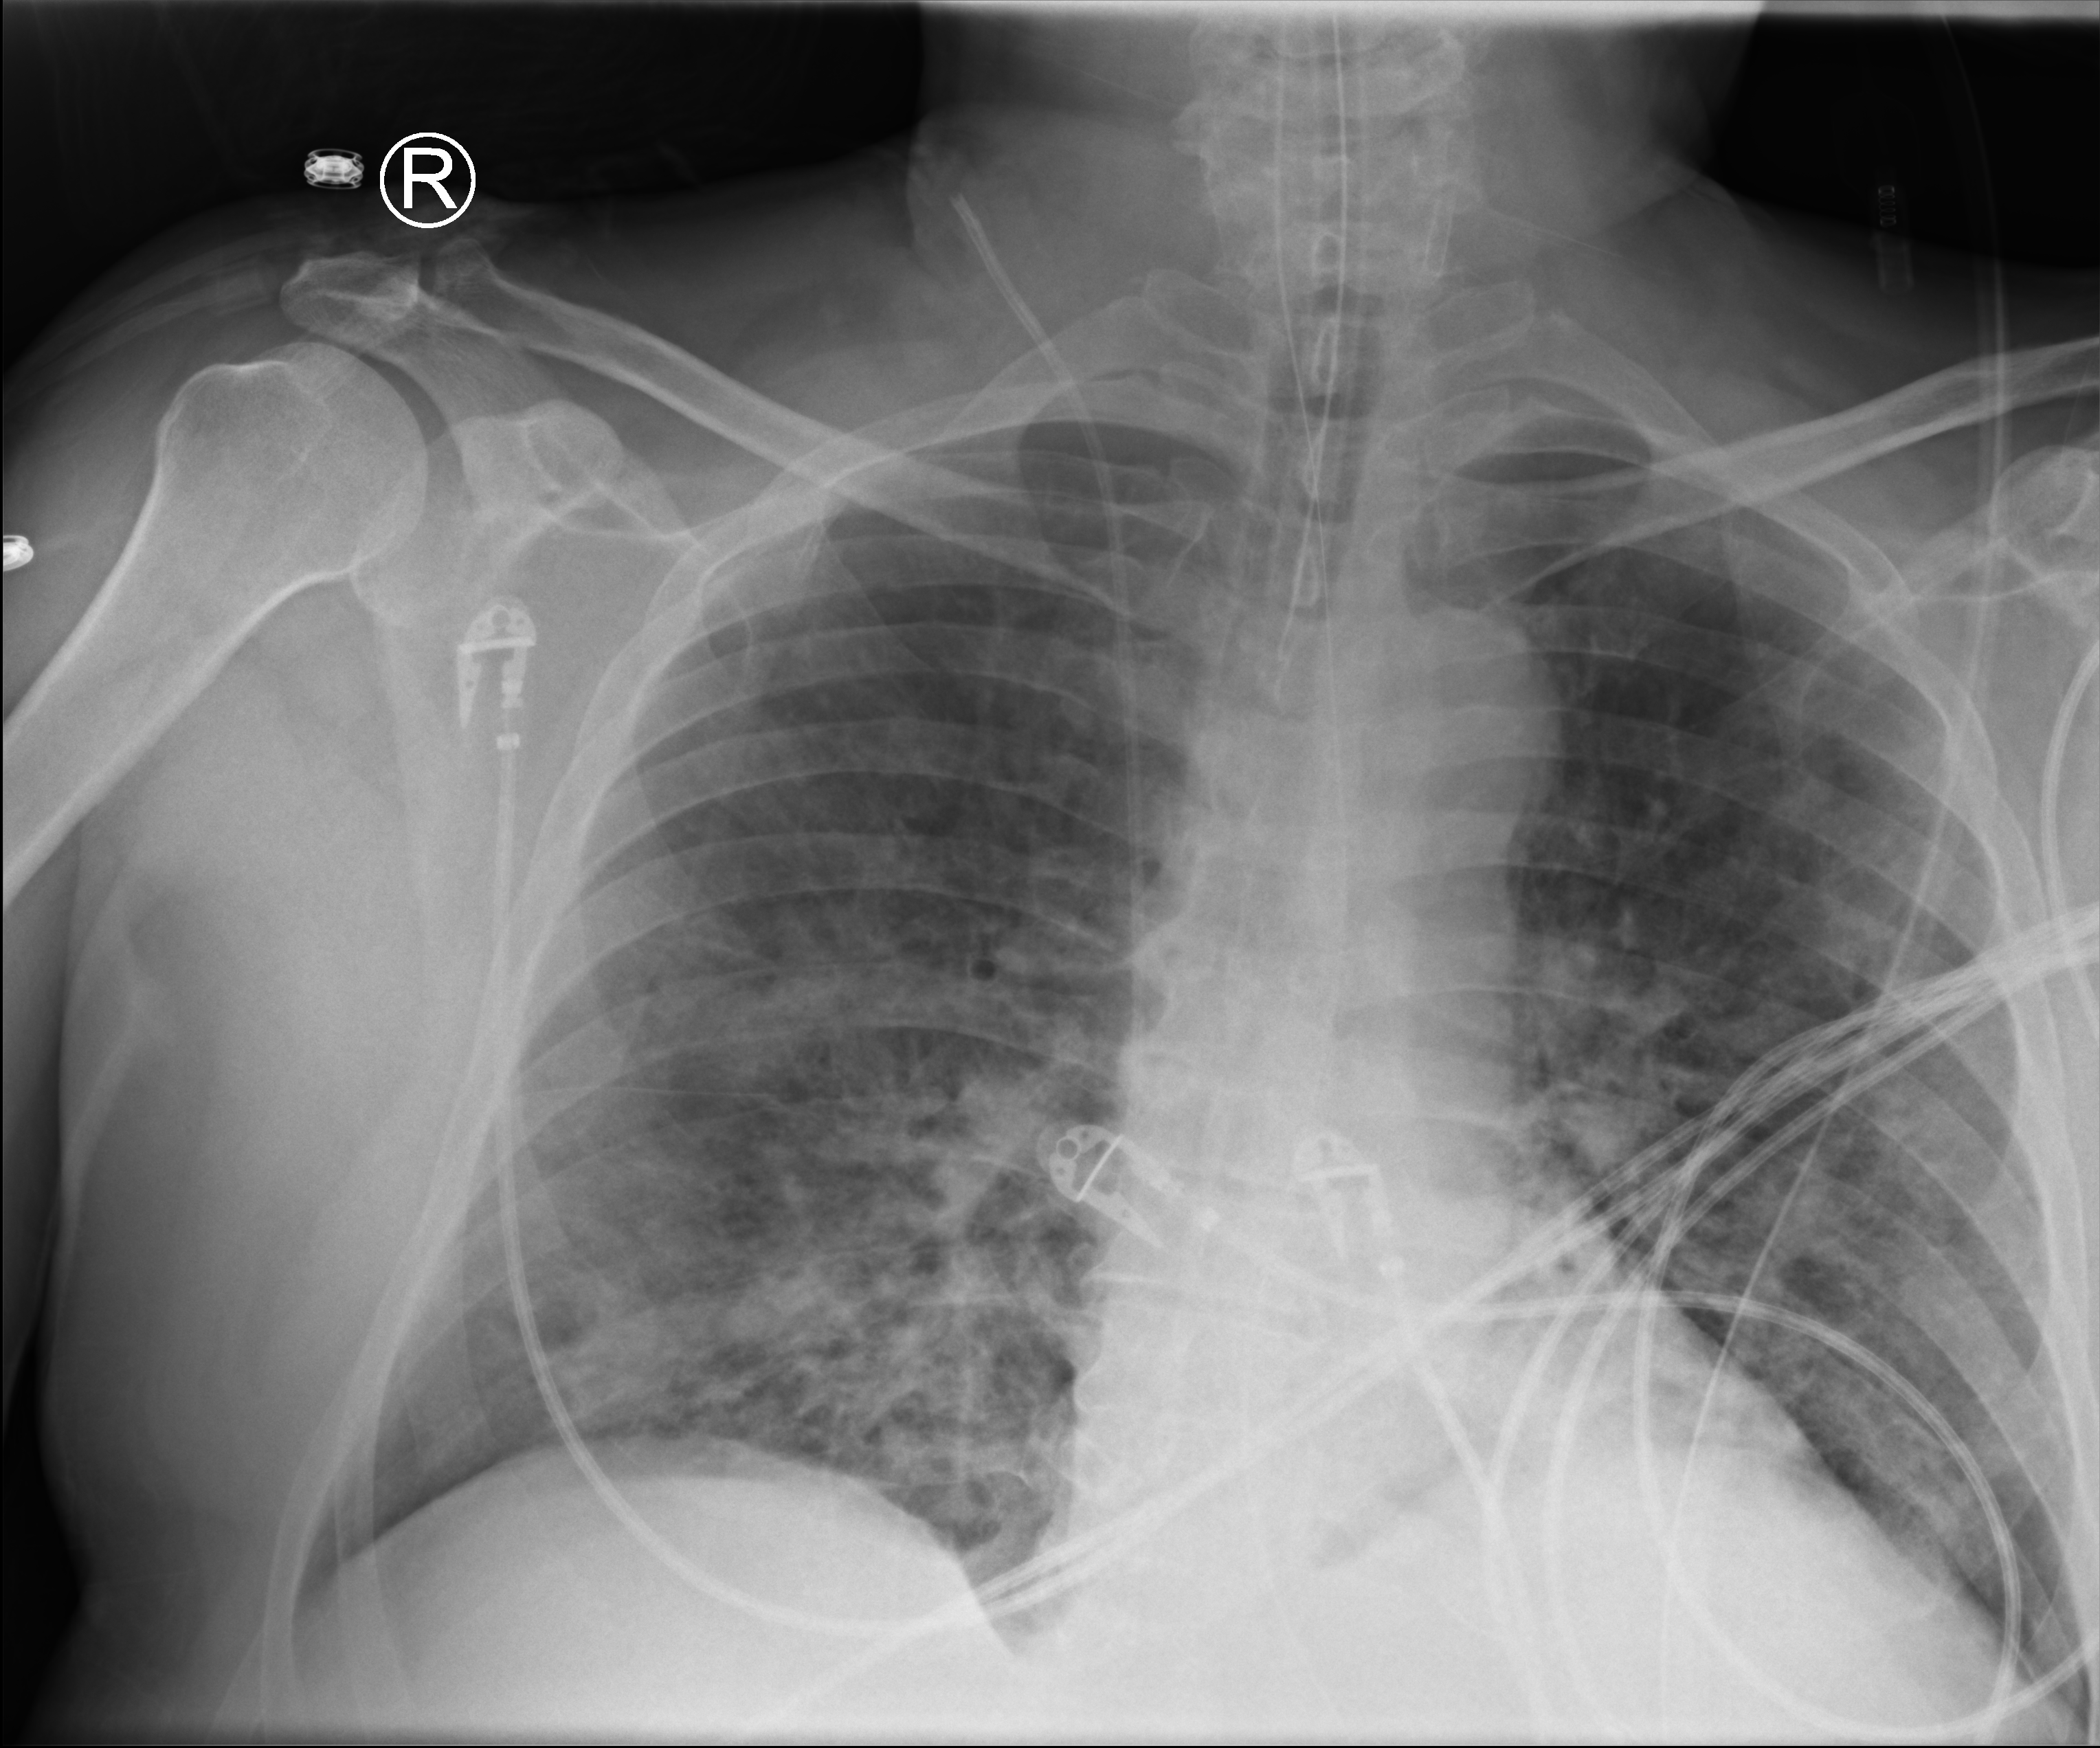
Chest X-ray (portable). Patient hospitalised with COVID-19; male, aged 60–74 years.
From the hospital-stay record, not from the radiograph (when in the stay this image was taken is not recorded): admitted to intensive care during this hospital stay: yes.